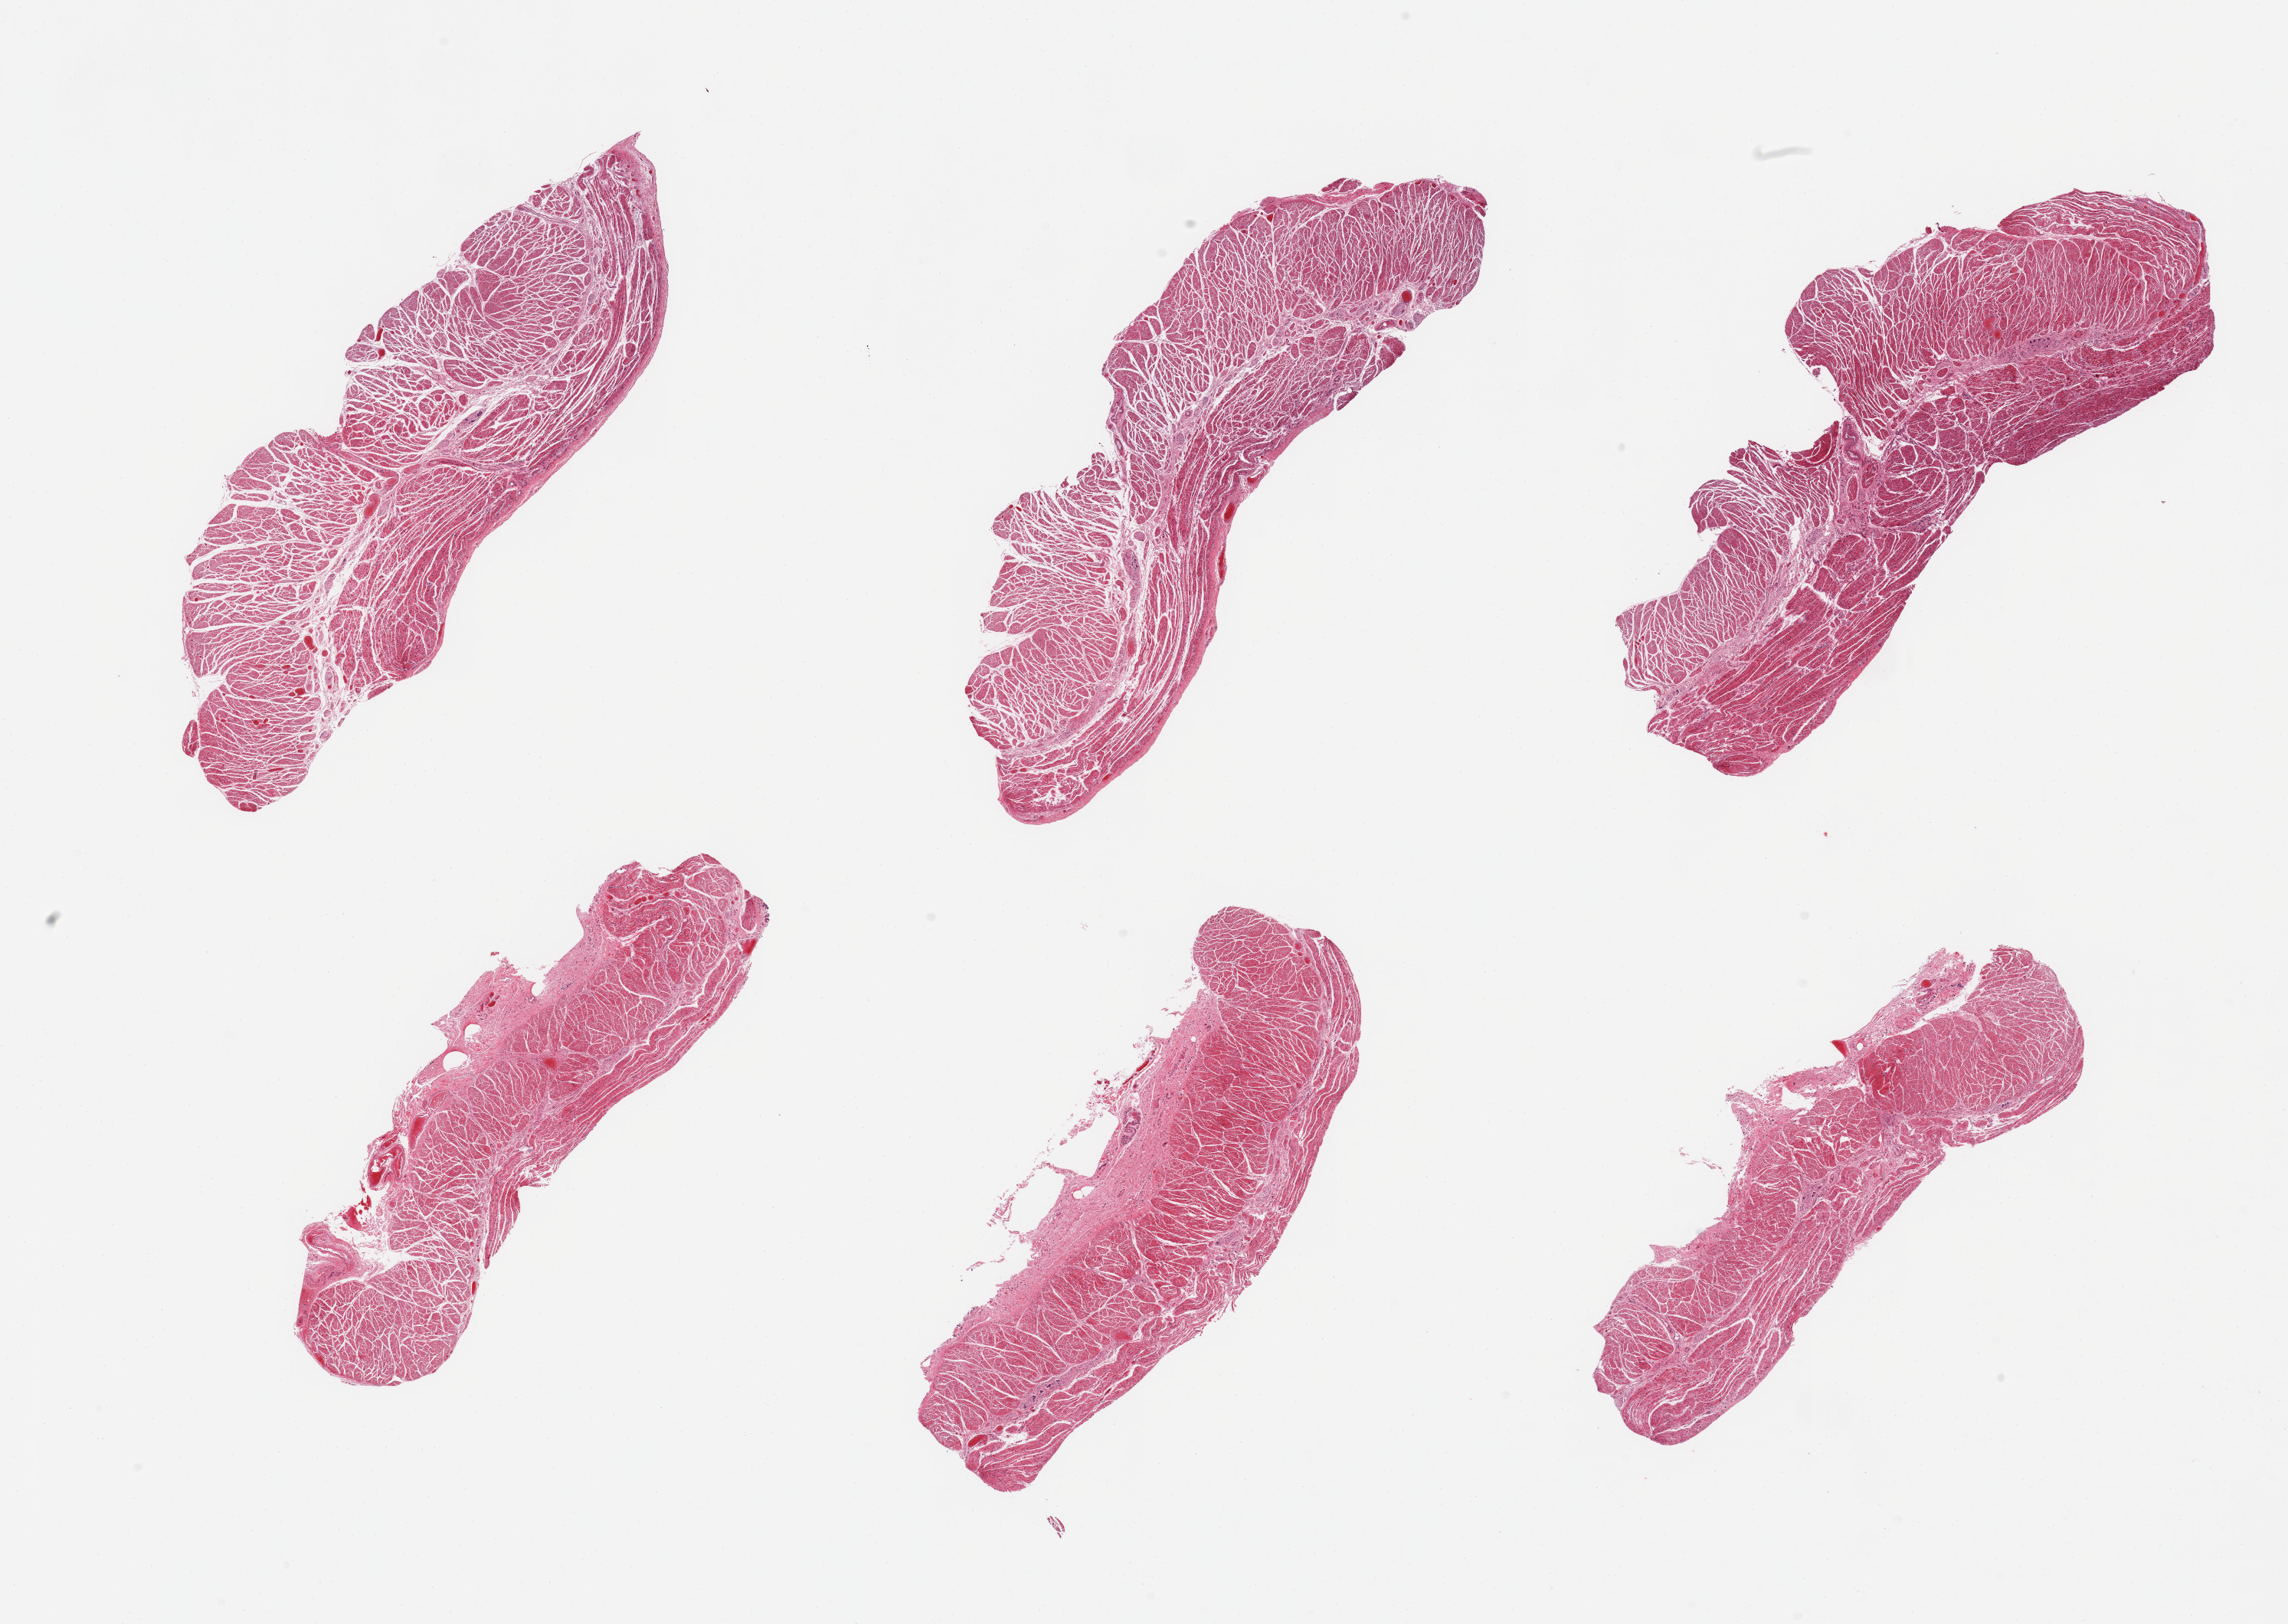
Whole-slide image, hematoxylin and eosin (H&E) stain, brightfield, whole scanned area (about 23.6 x 16.8 mm) shown as a low-resolution overview; PAXgene-fixed, paraffin-embedded tissue; target tissue: esophageal muscle; donor tissue sample. Male donor.
Review note (as recorded): 6 pieces; target muscularis.